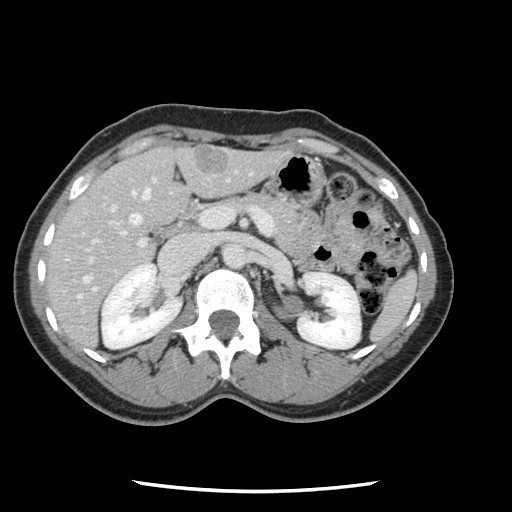
Contrast-enhanced abdominal CT, one axial slice. Slice 61 of 134 in the series (ordered by position). 120 kVp. Soft-tissue window (W 400 / L 40 HU). 512 × 512 image matrix. Female patient, age 43 years. From the clinical record (not read from this slice): diagnosis: colorectal cancer liver metastases, imaged before liver resection; multiple liver metastases: yes; largest metastasis: 3.4 cm.
Structures marked on this image (outlined manually by an expert reader):
- hepatic veins: bounding box [x1, y1, x2, y2] px = [78, 179, 156, 298]
- liver: [46, 146, 288, 349]
- planned liver remnant (the part of the liver to remain after resection): [47, 149, 184, 314]
- portal vein (with intrahepatic branches): [83, 171, 277, 312]
- liver metastasis: [194, 151, 230, 174]